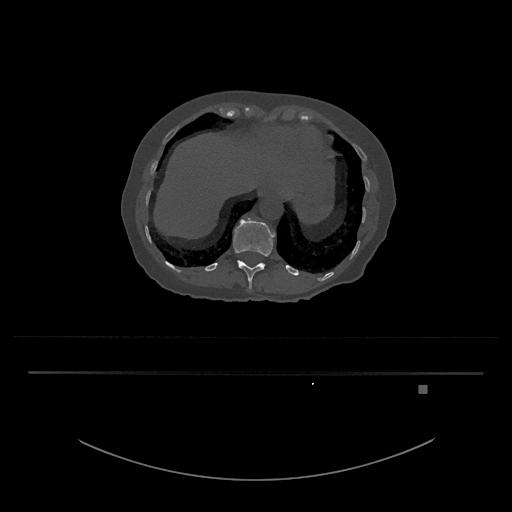
CT including the spine, one axial slice; position 607 of 797 along the scan axis; reconstruction kernel Br40s/3; 120 kVp; bone window (W 1800 / L 400 HU); 0.5 mm slice thickness; 512 × 512 image matrix, field of view 500 × 500 mm. Female patient, age 57 years. From the clinical record (not read from this slice): primary cancer: cervical.
Outlined on this slice (semi-automatically segmented with operator editing):
- T12 vertebra: bounding box <233,218,275,289> (left, top, right, bottom; pixels)